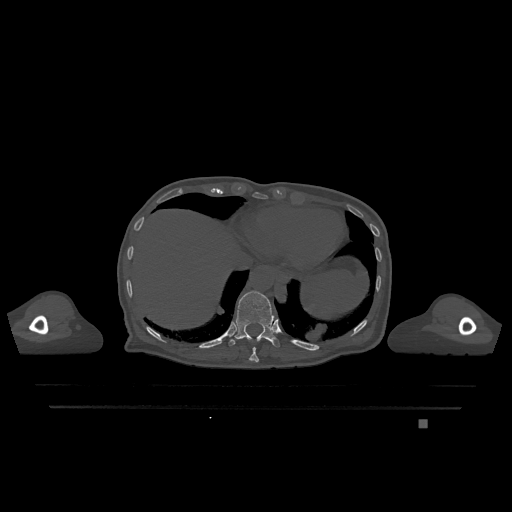
CT including the spine, one axial slice; position 604 of 1317 along the scan axis; bone window (W 1800 / L 400 HU); 0.5 mm slice thickness; 512 × 512 image matrix, field of view 500 × 500 mm. Female patient, age 74 years. From the clinical record (not read from this slice): primary cancer: lung; vertebrae with lytic lesions (as recorded): T1, T4, T5, T6, L4, L5.
Structures marked on this image (semi-automatically segmented with operator editing):
- T10 vertebra: bounding box <249,347,259,362> (left, top, right, bottom; pixels)
- T11 vertebra: <229,291,280,347>